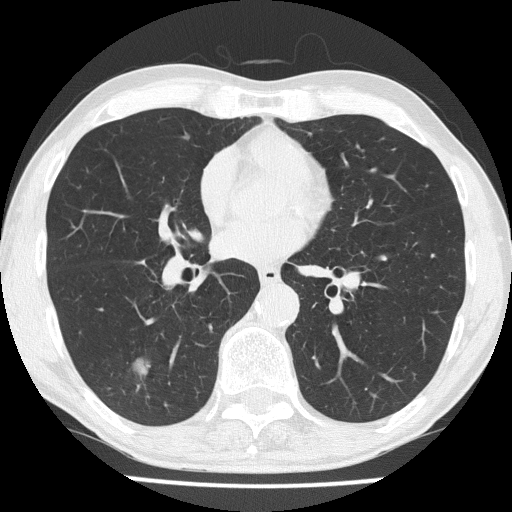
Low-dose screening chest CT, axial slice; third screening round (two years after baseline); lung window (W 1500 / L -600 HU); 2 mm slice thickness; slice 108 of 186 in the series; 512 × 512 image matrix, field of view 328 × 328 mm. Male, age 59 years at enrolment.
Expert reader's lesion annotation, box from (x=110, y=346) to (x=161, y=395) px. Screening reader's record for this exam (one nodule recorded; not confirmed to be the boxed lesion): non-calcified nodule or mass ≥4 mm, right lower lobe, 20 × 16 mm, smooth margins, soft tissue attenuation, pre-existing on the prior screen: no. Official screen result: positive, other. Later outcome: lung cancer diagnosed 25 days after this screen — small cell carcinoma, NOS, right lower lobe, stage IIA (AJCC 6th edition), 20 mm at pathology.